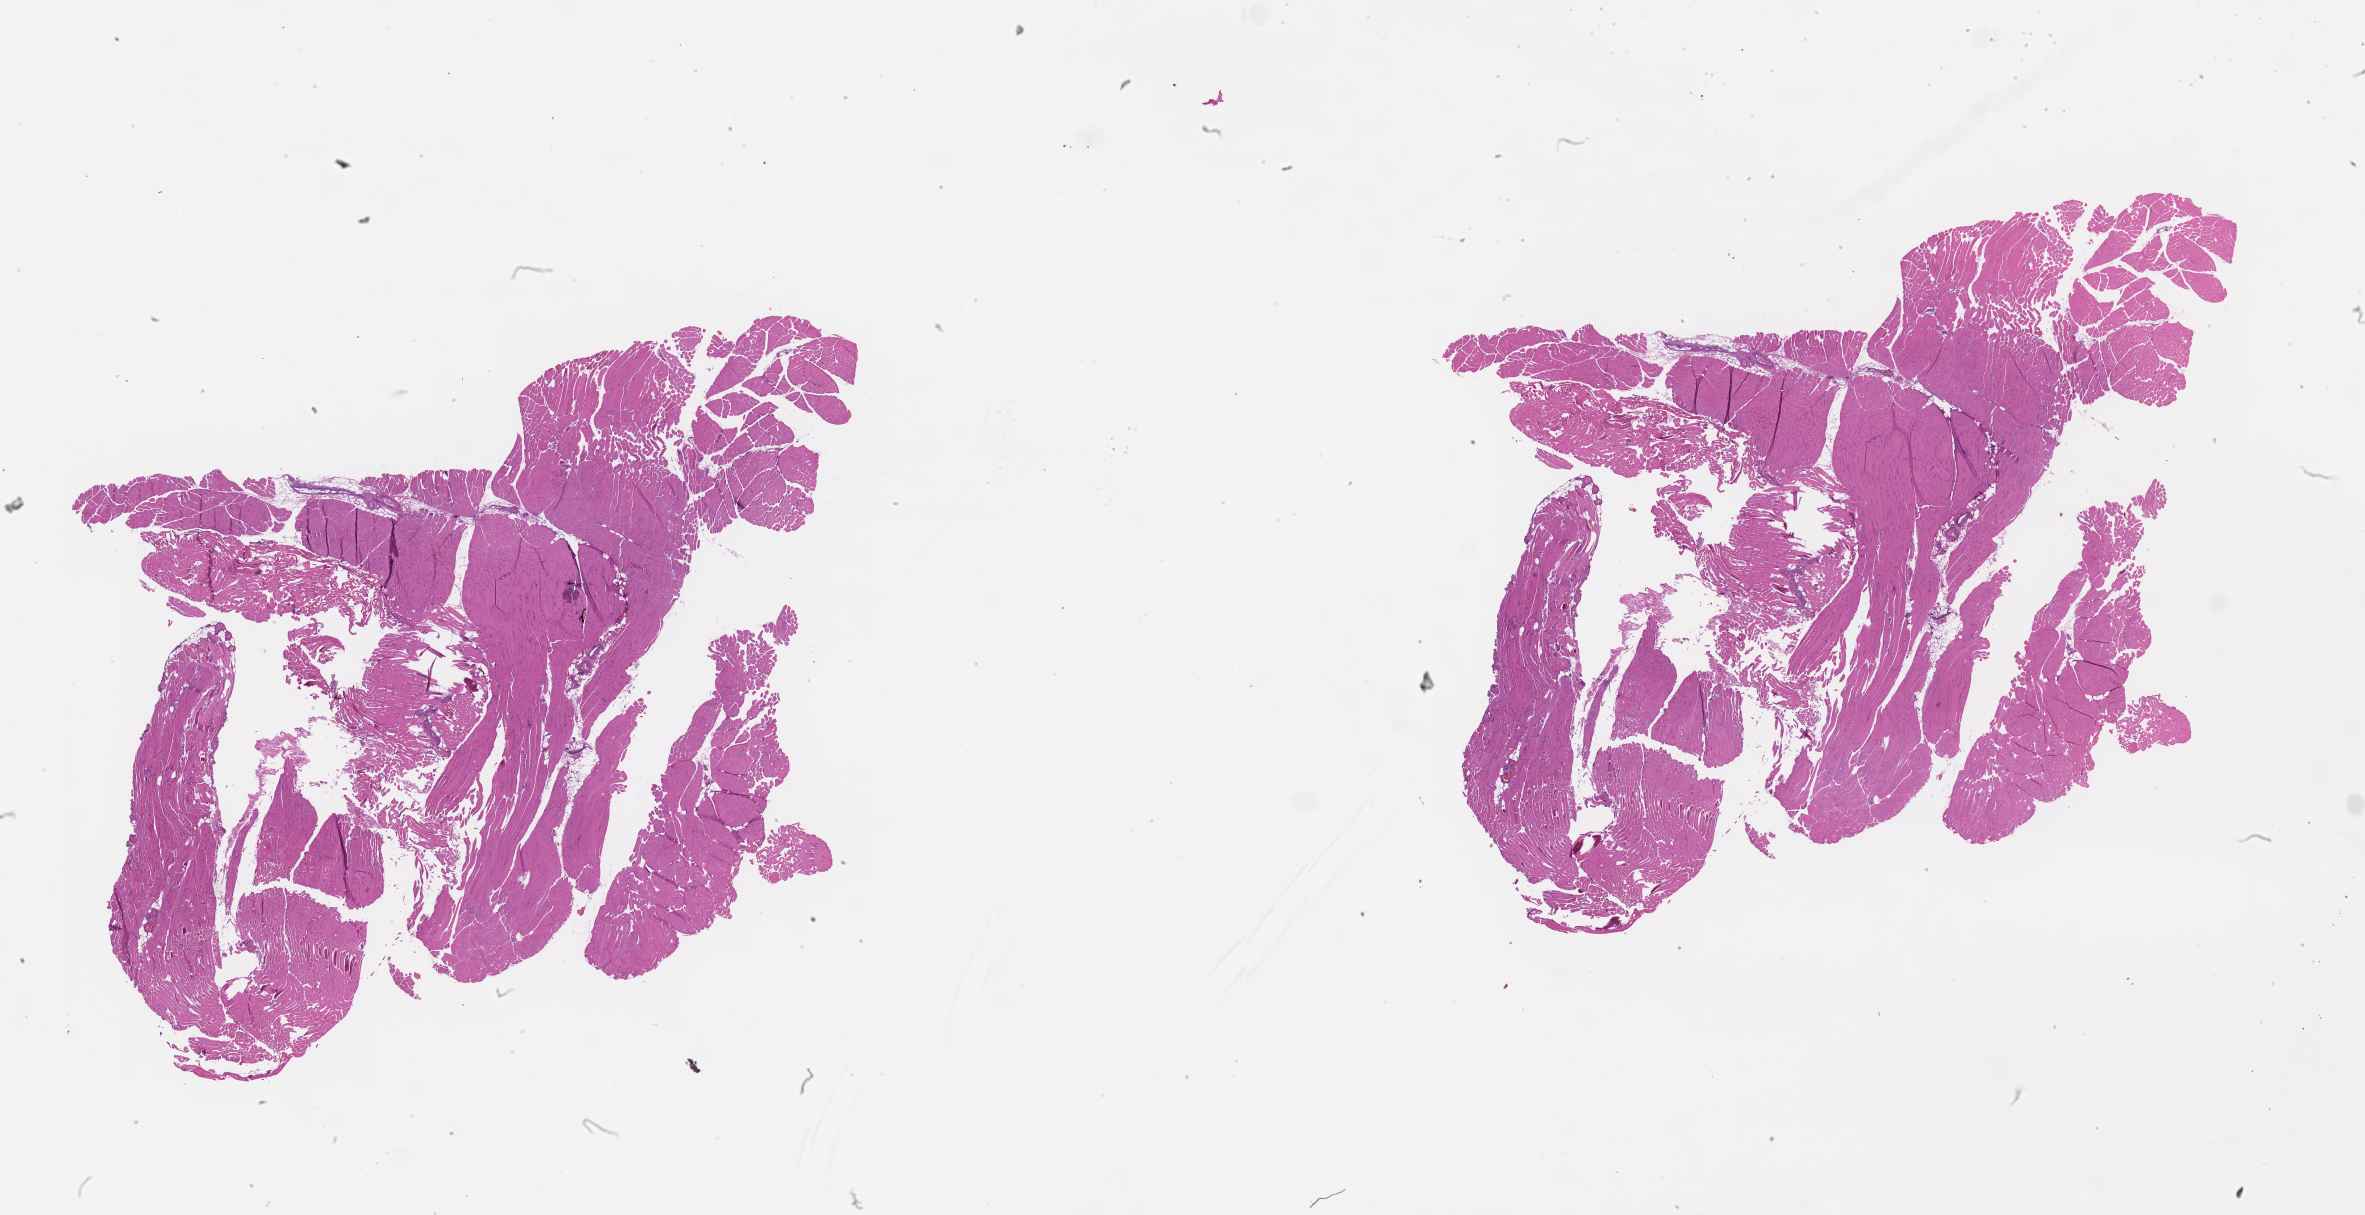
Digitized H&E-stained tissue section (whole slide), whole scanned area (about 38.1 x 19.6 mm, from a 20x scan) shown as a low-resolution overview.
Patient diagnosis (cohort enrolment): sarcoma (site not recorded at cohort level).